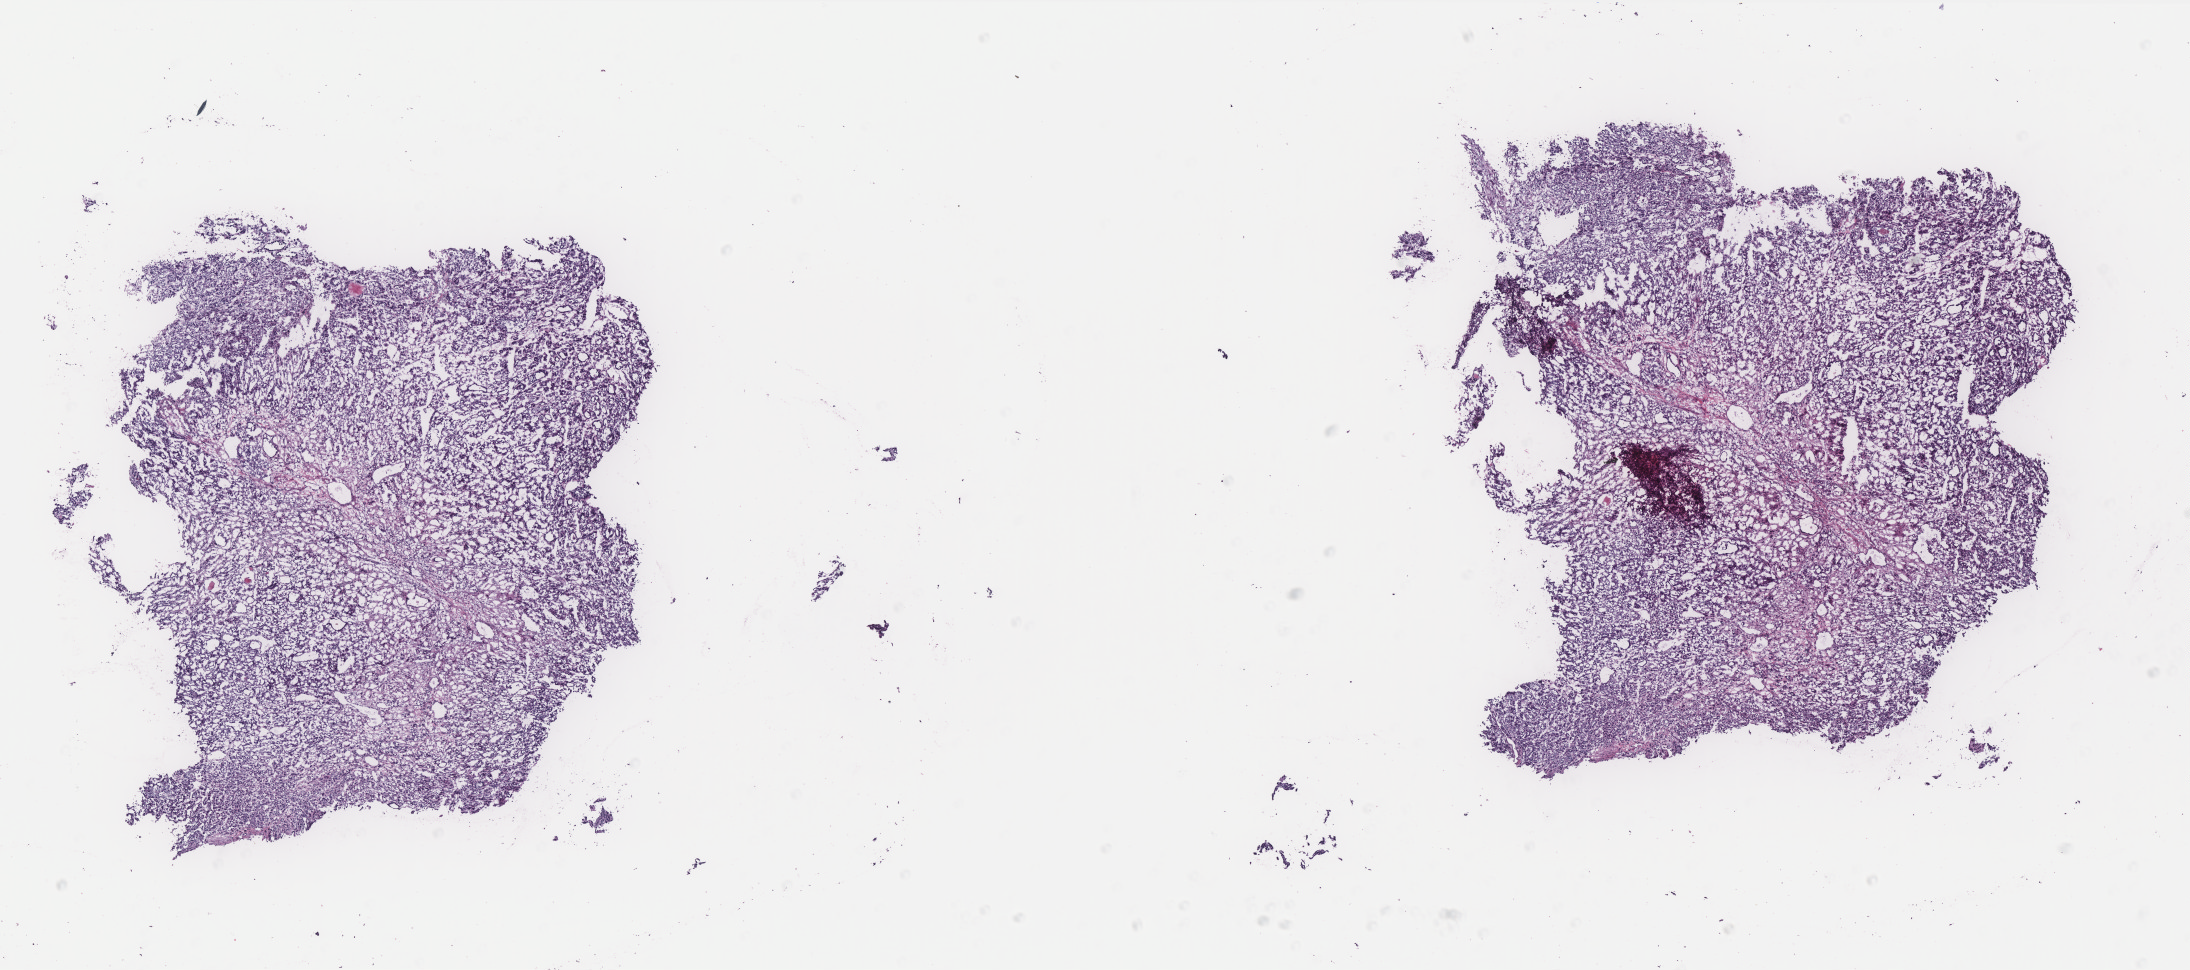
H&E whole-slide image, a low-resolution overview of the entire scanned area, about 17.6 x 7.8 mm (slide scanned at 40x), frozen section from the top of the tissue portion, sample: primary tumour, thyroid. Patient: female, age at initial diagnosis 54 years.
Histologic diagnosis: Follicular carcinoma, minimally invasive (thyroid gland).